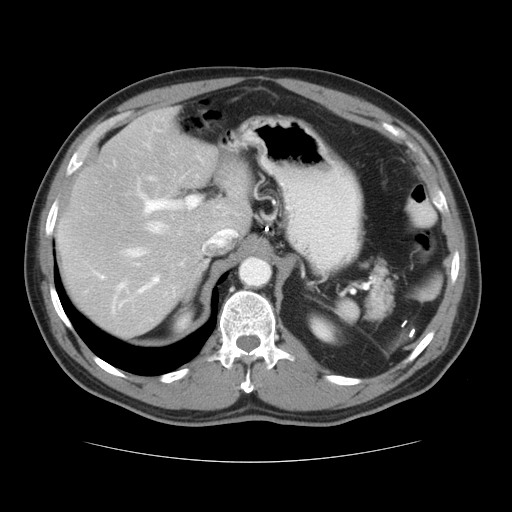
Contrast-enhanced abdominal CT, one axial slice. Position 24 of 37 along the scan axis. Reconstruction kernel STANDARD. 120 kVp. Intravenous contrast given. Soft-tissue window (W 400 / L 40 HU). 5 mm slice thickness. 512 × 512 image matrix, field of view 374 × 374 mm. Male patient, age 66 years. Case-level facts recorded for this patient, not image findings: diagnosis: colorectal cancer liver metastases, imaged before liver resection; multiple liver metastases: yes; largest metastasis: 1.6 cm; disease in both lobes: yes.
Outlined on this slice (manually delineated by an expert):
- hepatic veins: bounding box (x1, y1, x2, y2) in pixels: (118, 177, 238, 291)
- liver: (55, 107, 253, 338)
- planned liver remnant (the part of the liver to remain after resection): (54, 147, 254, 339)
- portal vein (with intrahepatic branches): (94, 184, 200, 293)
- liver metastasis: (112, 194, 130, 212)